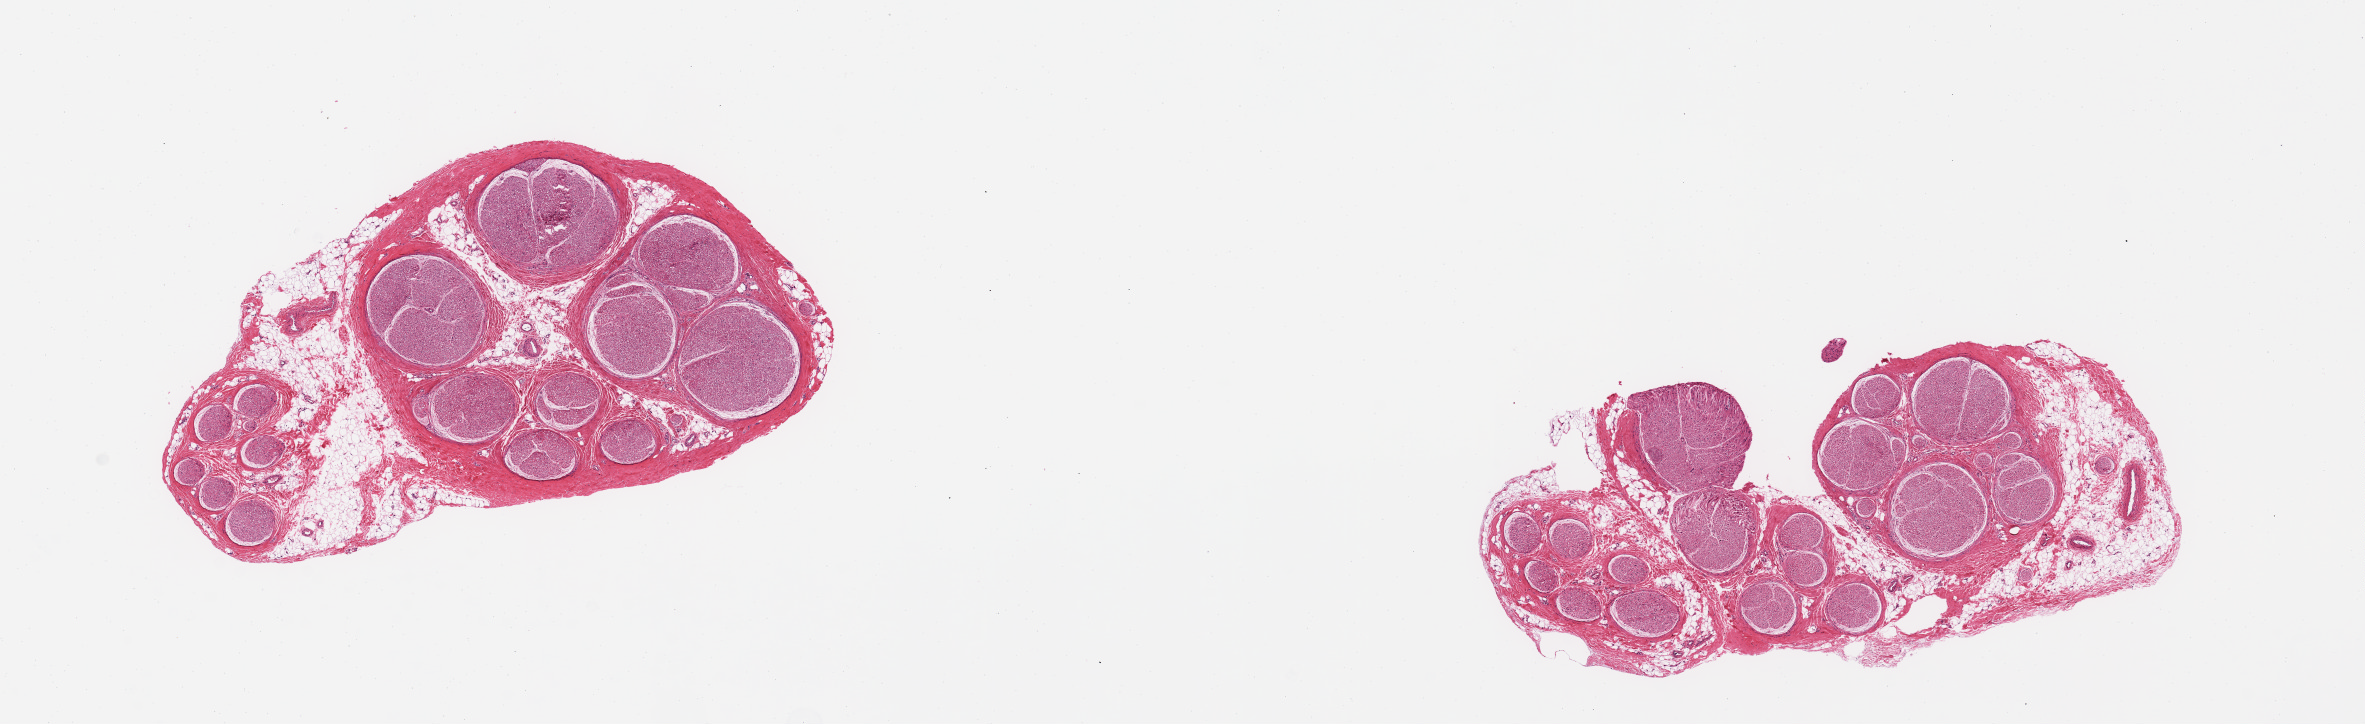
H&E whole-slide image, whole scanned area (about 18.7 x 5.7 mm, slide scanned at 20x) shown as a low-resolution overview, PAXgene-fixed, paraffin-embedded tissue, section of tibial nerve (target tissue), donor tissue sample.
- pathologist's review note for this sample: 2 pieces; no llesions